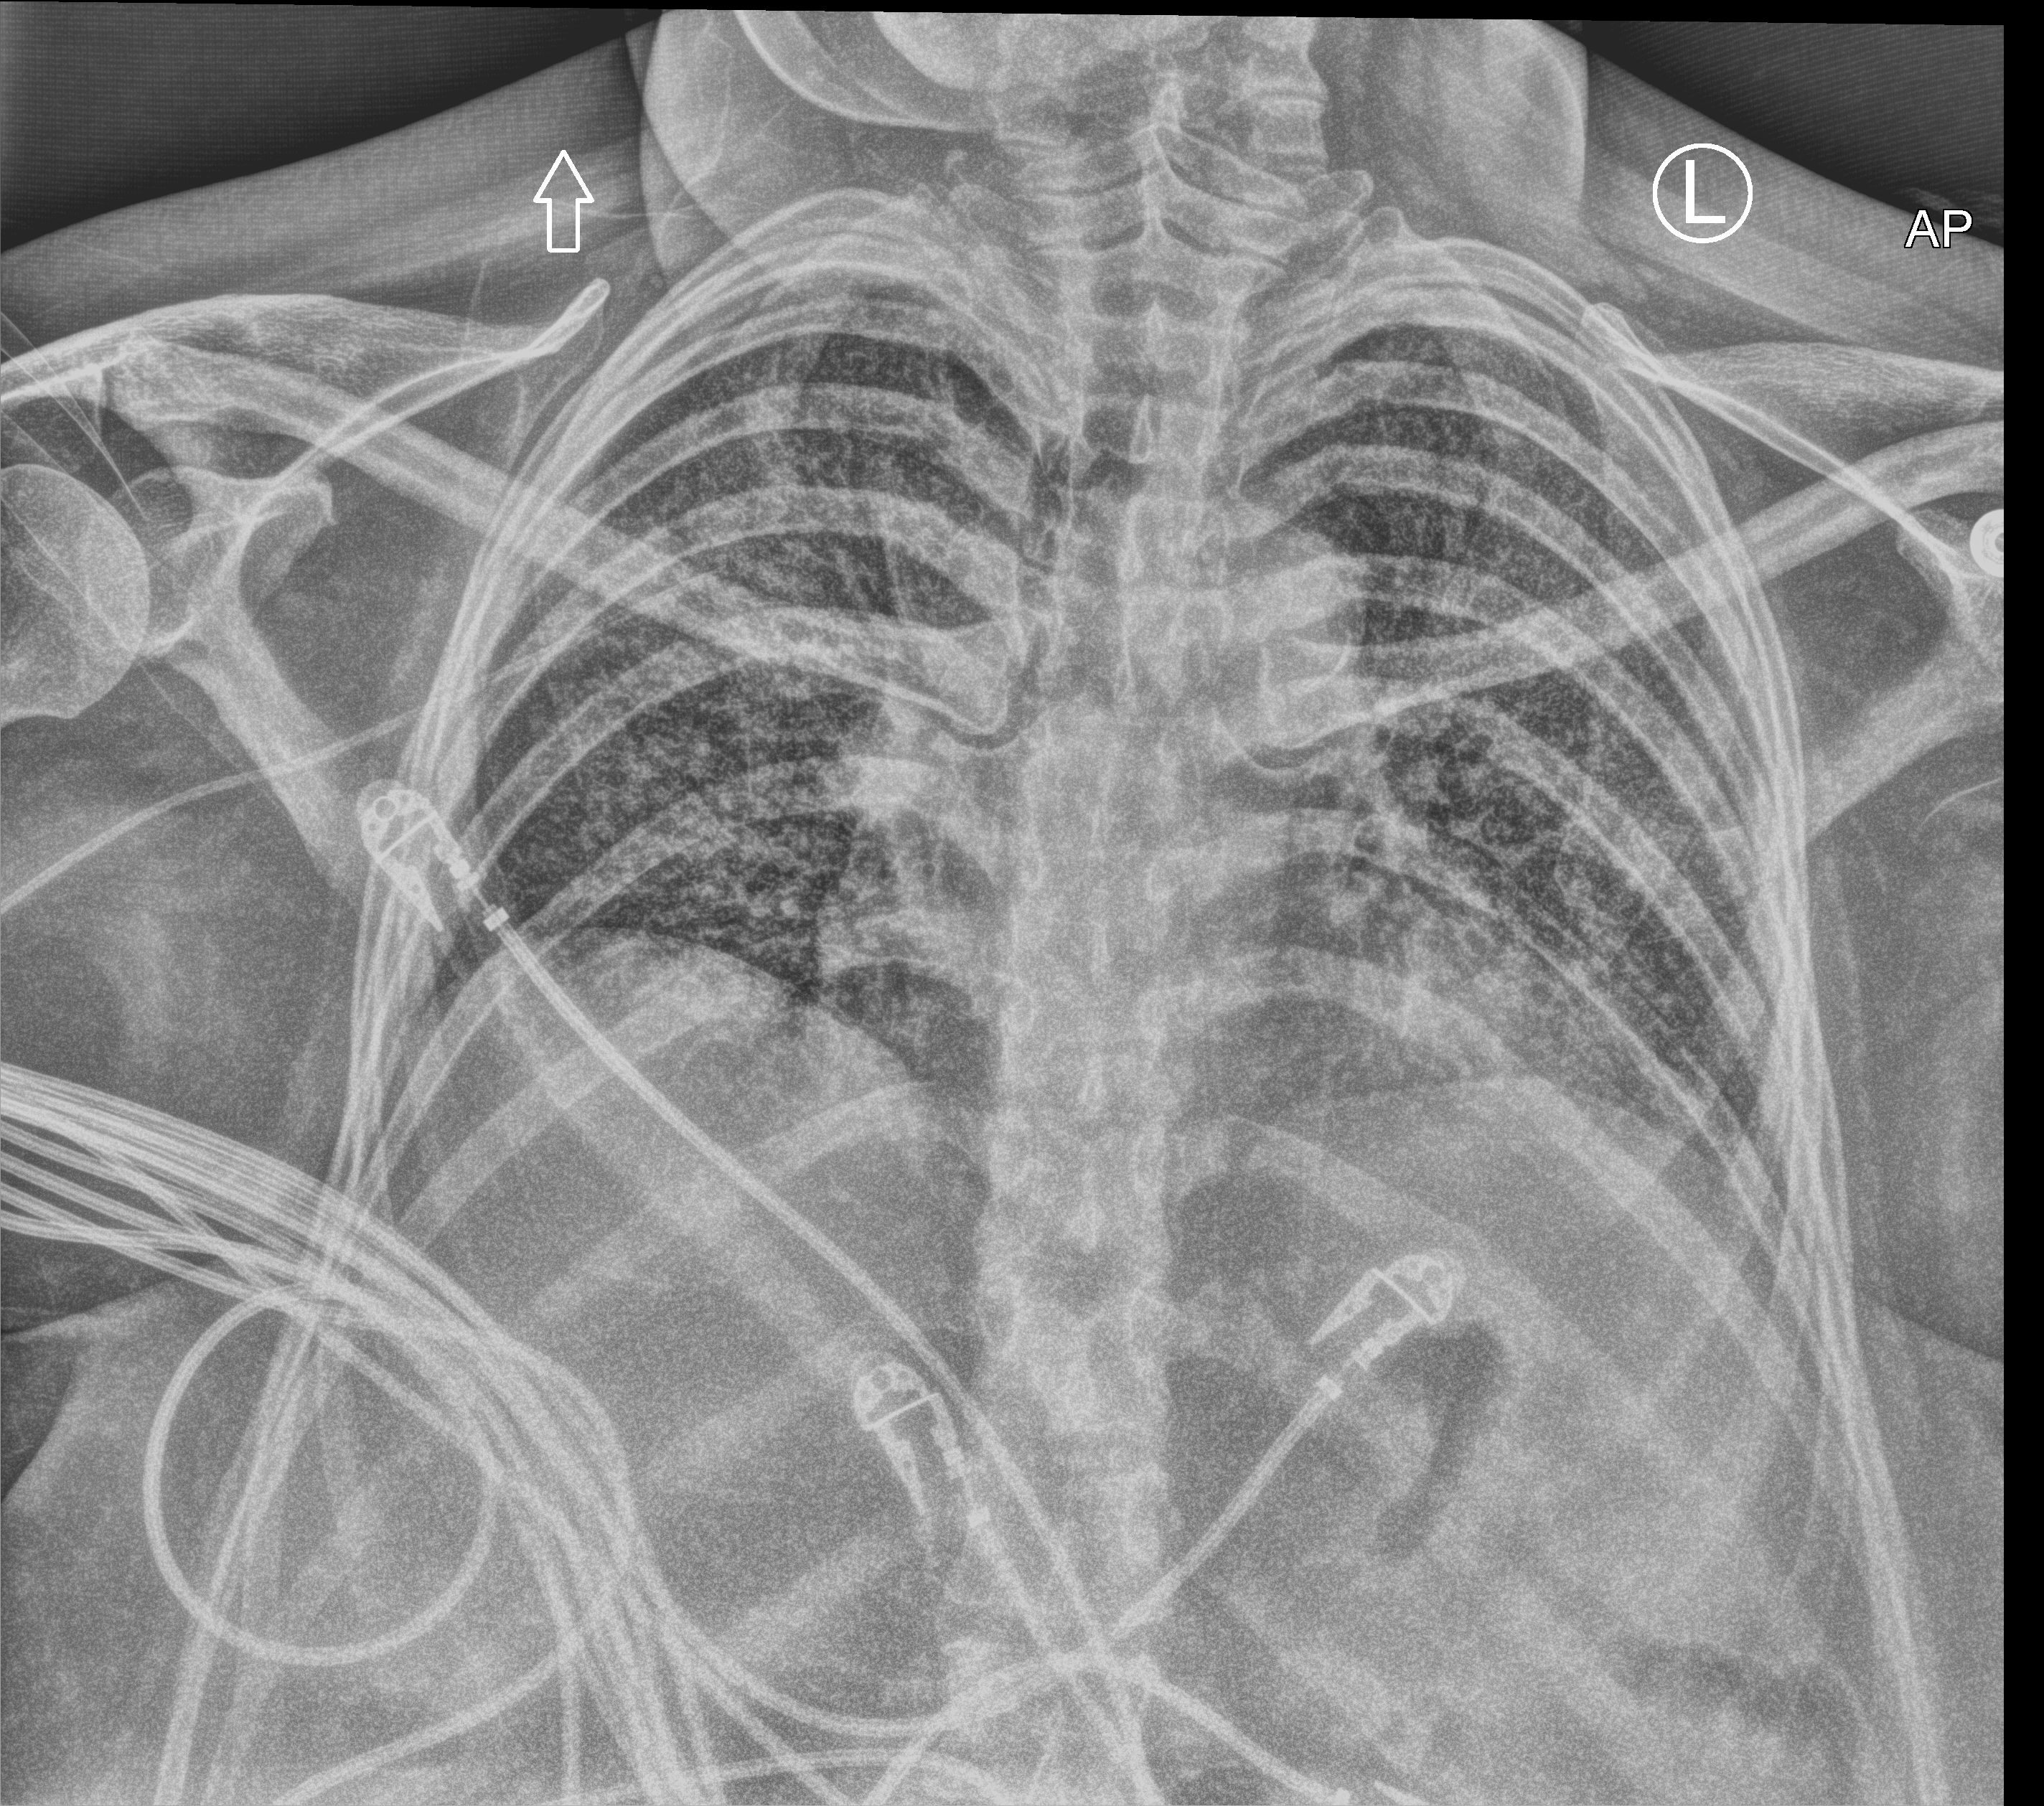
Chest X-ray (portable); anteroposterior (AP) projection. Female patient hospitalised with COVID-19, age 18–59 years.
From the hospital-stay record, not from the radiograph (when in the stay this image was taken is not recorded):
- mechanically ventilated during this hospital stay: yes